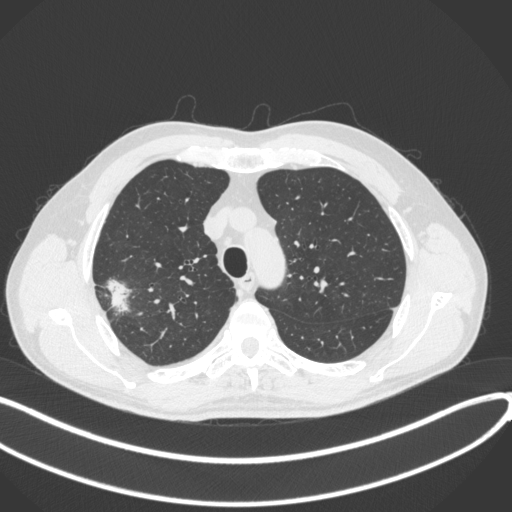
Chest CT, one axial slice. Position 319 of 381 along the scan axis. Reconstruction kernel B31f. Lung window (W 1500 / L -600 HU). 1 mm slice thickness. 512 × 512 image matrix, field of view 400 × 400 mm. Patient: male, 62 years. From the clinical record (not read from this slice): clinical TNM (as recorded): T1c N0 M0; histopathological grade: G2-3.
Annotated regions visible in this slice (bounding box drawn by a radiologist):
- lung tumour (recorded histology: adenocarcinoma): bounding box (x1, y1, x2, y2) in pixels: (101, 274, 137, 317)